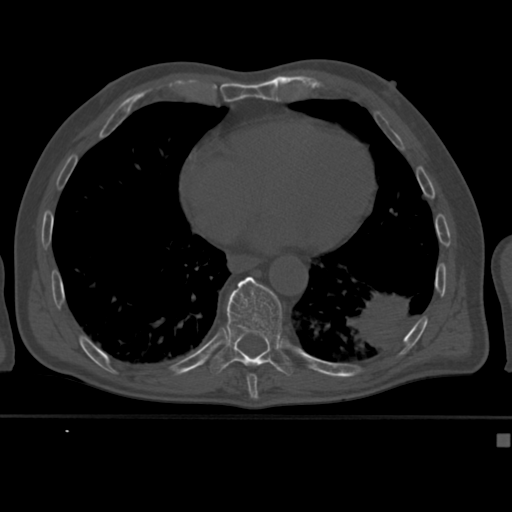
CT including the spine, one axial slice; slice 233 of 430 in the series (ordered by position); reconstruction kernel Br40s; bone window (W 1800 / L 400 HU); 1.5 mm slice thickness; 512 × 512 image matrix. Patient: male, 64 years. Case-level facts recorded for this patient, not image findings: primary cancer: uterus; vertebrae with lytic lesions (as recorded): T1, T4, T5, T7, L5.
Structures marked on this image (semi-automatically segmented with operator editing):
- T10 vertebra: bounding box (x1, y1, x2, y2) in pixels: (209, 276, 295, 377)
- T9 vertebra: (247, 374, 258, 382)